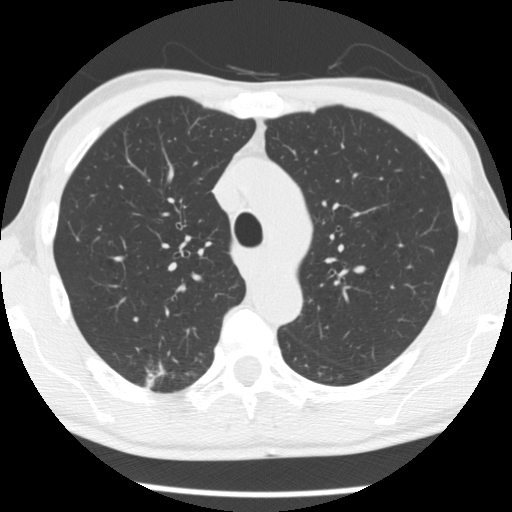
Axial slice from a low-dose chest CT screening exam; baseline screening round; lung window (W 1500 / L -600 HU); 2.5 mm slice thickness; slice 80 of 277 in the series. Male, age 66 years at enrolment. Former smoker at enrolment.
Expert-annotated lung lesion, bounding box (x1, y1, x2, y2) in pixels: (133, 356, 188, 398). The screening reader recorded 4 non-calcified nodules or masses ≥4 mm on this exam (right upper lobe, right upper lobe, right upper lobe, left lower lobe); which of them this box marks is not recorded. Official screen result: positive, change unspecified: nodule(s) >= 4 mm or enlarging nodule(s), mass(es), or other non-specific abnormalities suspicious for lung cancer. Later outcome: lung cancer diagnosed 503 days after this screen — adenocarcinoma, NOS, right upper lobe, undifferentiated (G4), stage IA (AJCC 6th edition), 20 mm at pathology.